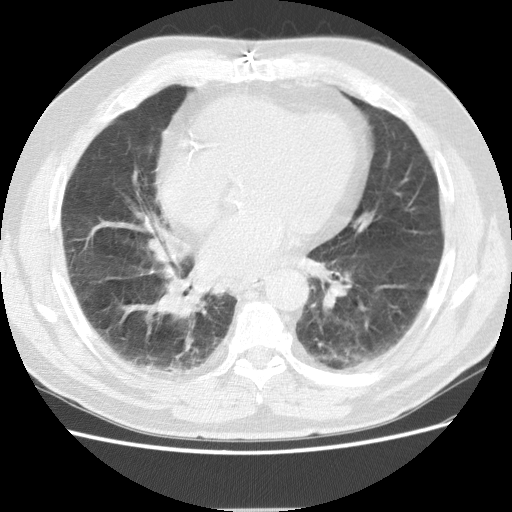
Chest CT (low-dose screening protocol), one axial image; first (baseline) screen; lung window (W 1500 / L -600 HU); 2.5 mm slice thickness; standard (soft-tissue) reconstruction kernel (STANDARD); 120 kVp; 512 × 512 image matrix. Male, age 72 years at enrolment. Former smoker at enrolment.
Lesion marked by an expert reader, box from (x=142, y=227) to (x=196, y=267) px. No non-calcified nodule or mass ≥4 mm was recorded by the screening reader at this exam. Lung cancer was diagnosed 163 days after this screen: adenocarcinoma, NOS, right middle lobe, stage IIIB (AJCC 6th edition), 27 mm at pathology.